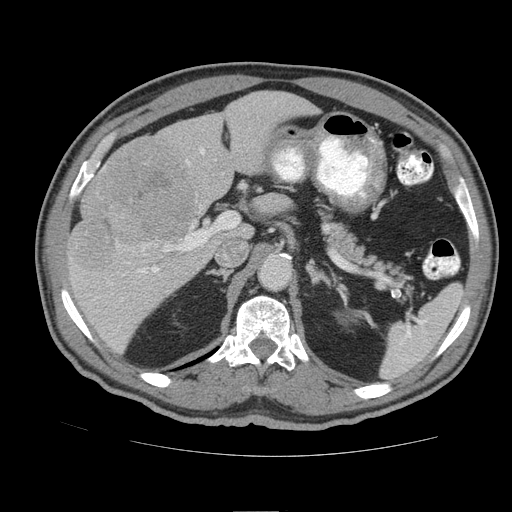
Contrast-enhanced abdominal CT (liver protocol), one axial slice. Slice 54 of 105 in the series (ordered by position). Soft-tissue window (W 400 / L 40 HU). 512 × 512 image matrix. Case-level facts recorded for this patient, not image findings: diagnosis: hepatocellular carcinoma (patient treated with transarterial chemoembolisation; whether this scan precedes or follows treatment is not stated here); TNM stage (as recorded): Stage-IIIB; Child-Pugh class: A.
Structures marked on this image (semi-automatic segmentation, software-assisted and operator-edited):
- liver parenchyma outside the tumour (the mass and vessels are separate outlines, so this box may not span the whole liver): bounding box [x1, y1, x2, y2] px = [66, 90, 318, 352]
- mass: [72, 141, 198, 269]
- liver vessels: [128, 149, 204, 274]